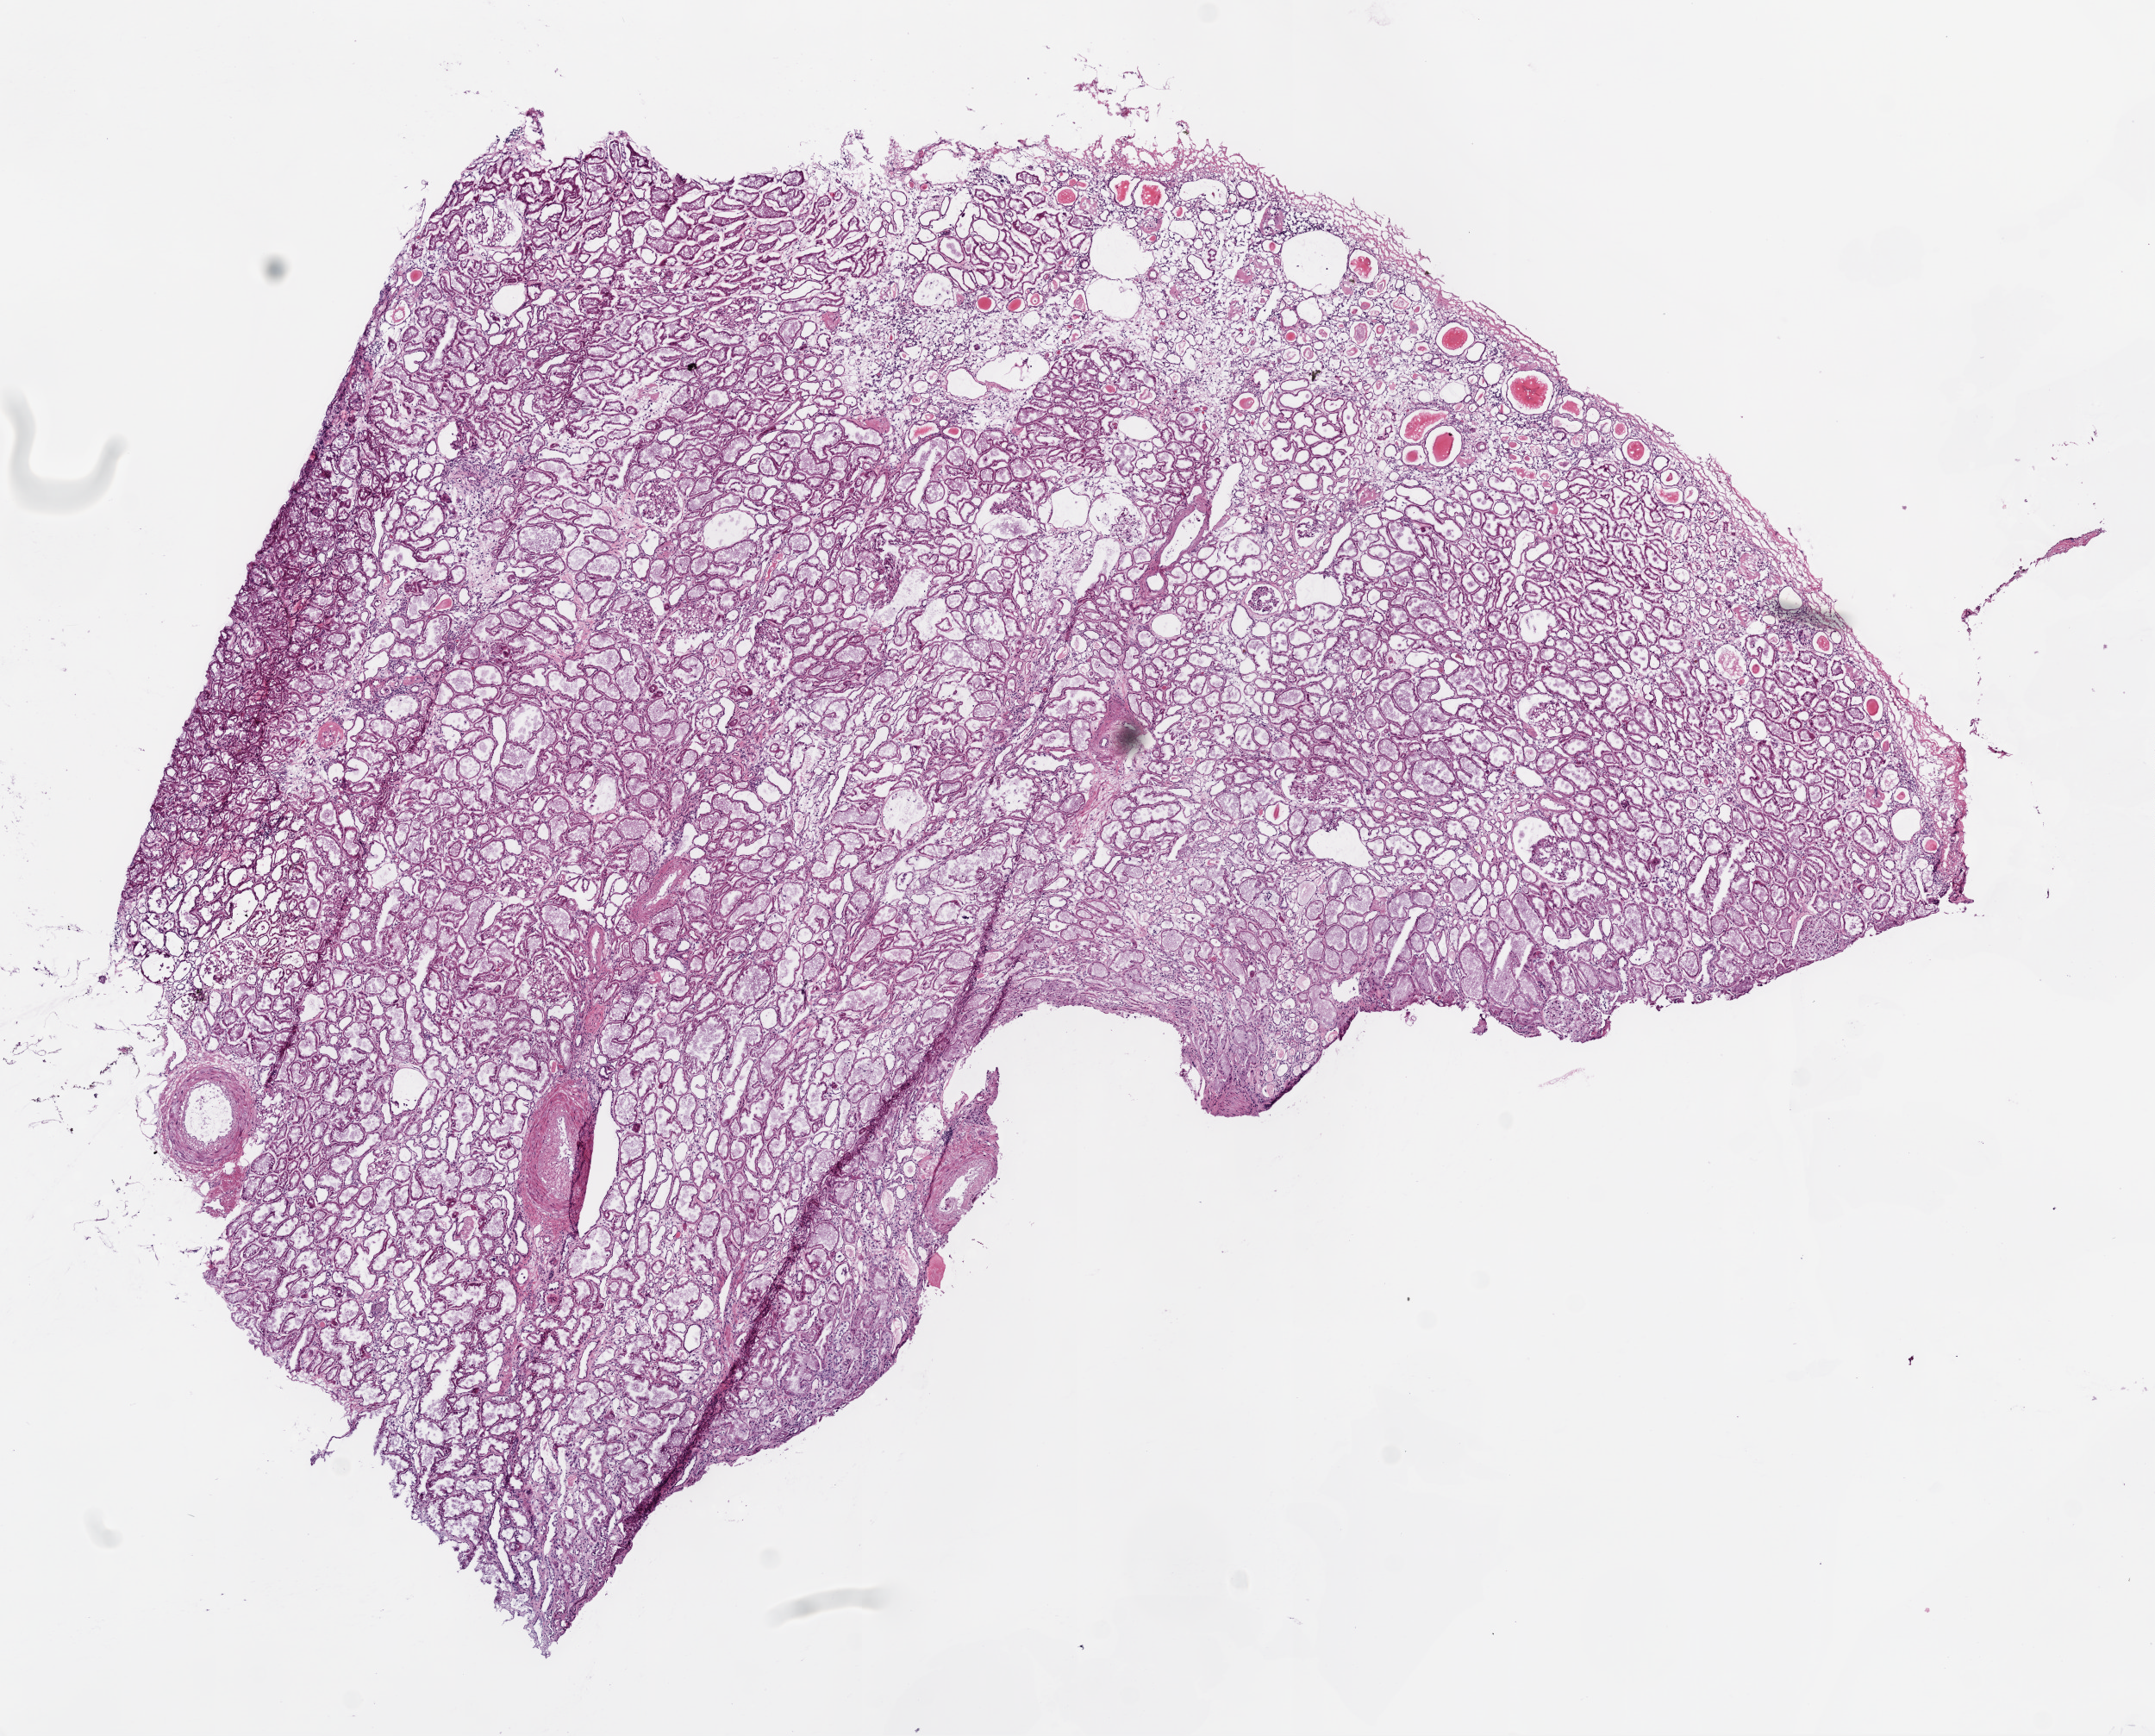
H&E-stained whole-slide image — low-resolution overview of the scanned area, about 10.0 x 8.1 mm (slide scanned at 20x), frozen section from the bottom of the tissue portion, solid tissue normal (non-tumour tissue) sample from the kidney. Male, age 52 years at initial diagnosis.
- this section: solid tissue normal (non-tumour) sample from the same patient
- patient diagnosis: Clear cell adenocarcinoma, NOS